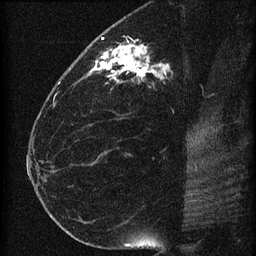
Breast MRI (dynamic contrast-enhanced), one sagittal slice; slice 32 of 60 in the series (ordered by position); dynamic contrast-enhanced series, image 2 of 4 at this slice position (ordered by acquisition); 1.5 T; TE 4.2 ms, TR 22.7 ms; 256 × 256 image matrix, field of view 180 × 180 mm. Patient: female, 35 years. Case-level facts recorded for this patient, not image findings: setting: breast cancer imaged before/during neoadjuvant chemotherapy; receptor status: HR-positive, HER2-negative.
Annotated regions visible in this slice (semi-automatic segmentation, software-assisted and operator-edited):
- analysis volume of interest (the breast-tissue region the enhancement analysis was run in; not a lesion): bounding box <69,27,199,112> (left, top, right, bottom; pixels)
- tumour enhancement mask (voxels above the 90 % enhancement threshold inside the analysis volume of interest): <87,37,167,84>